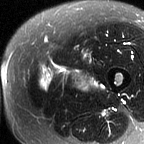
MRI of an extremity soft-tissue mass, one axial slice. Position 16 of 60 along the scan axis. T2-weighted fat-saturated. MR volume resampled by the dataset authors to the PET/CT grid (not the native acquisition matrix). 144 × 144 image matrix, field of view 141 × 141 mm. Female patient. Case-level facts recorded for this patient, not image findings: histological type: pleiomorphic leiomyosarcoma; grade: intermediate; site of the primary tumour: left thigh.
Outlined on this slice (expert contour drawn on MRI and transferred to this co-registered scan by the dataset authors):
- gross tumour volume including surrounding oedema: bounding box [x1, y1, x2, y2] px = [40, 65, 103, 91]